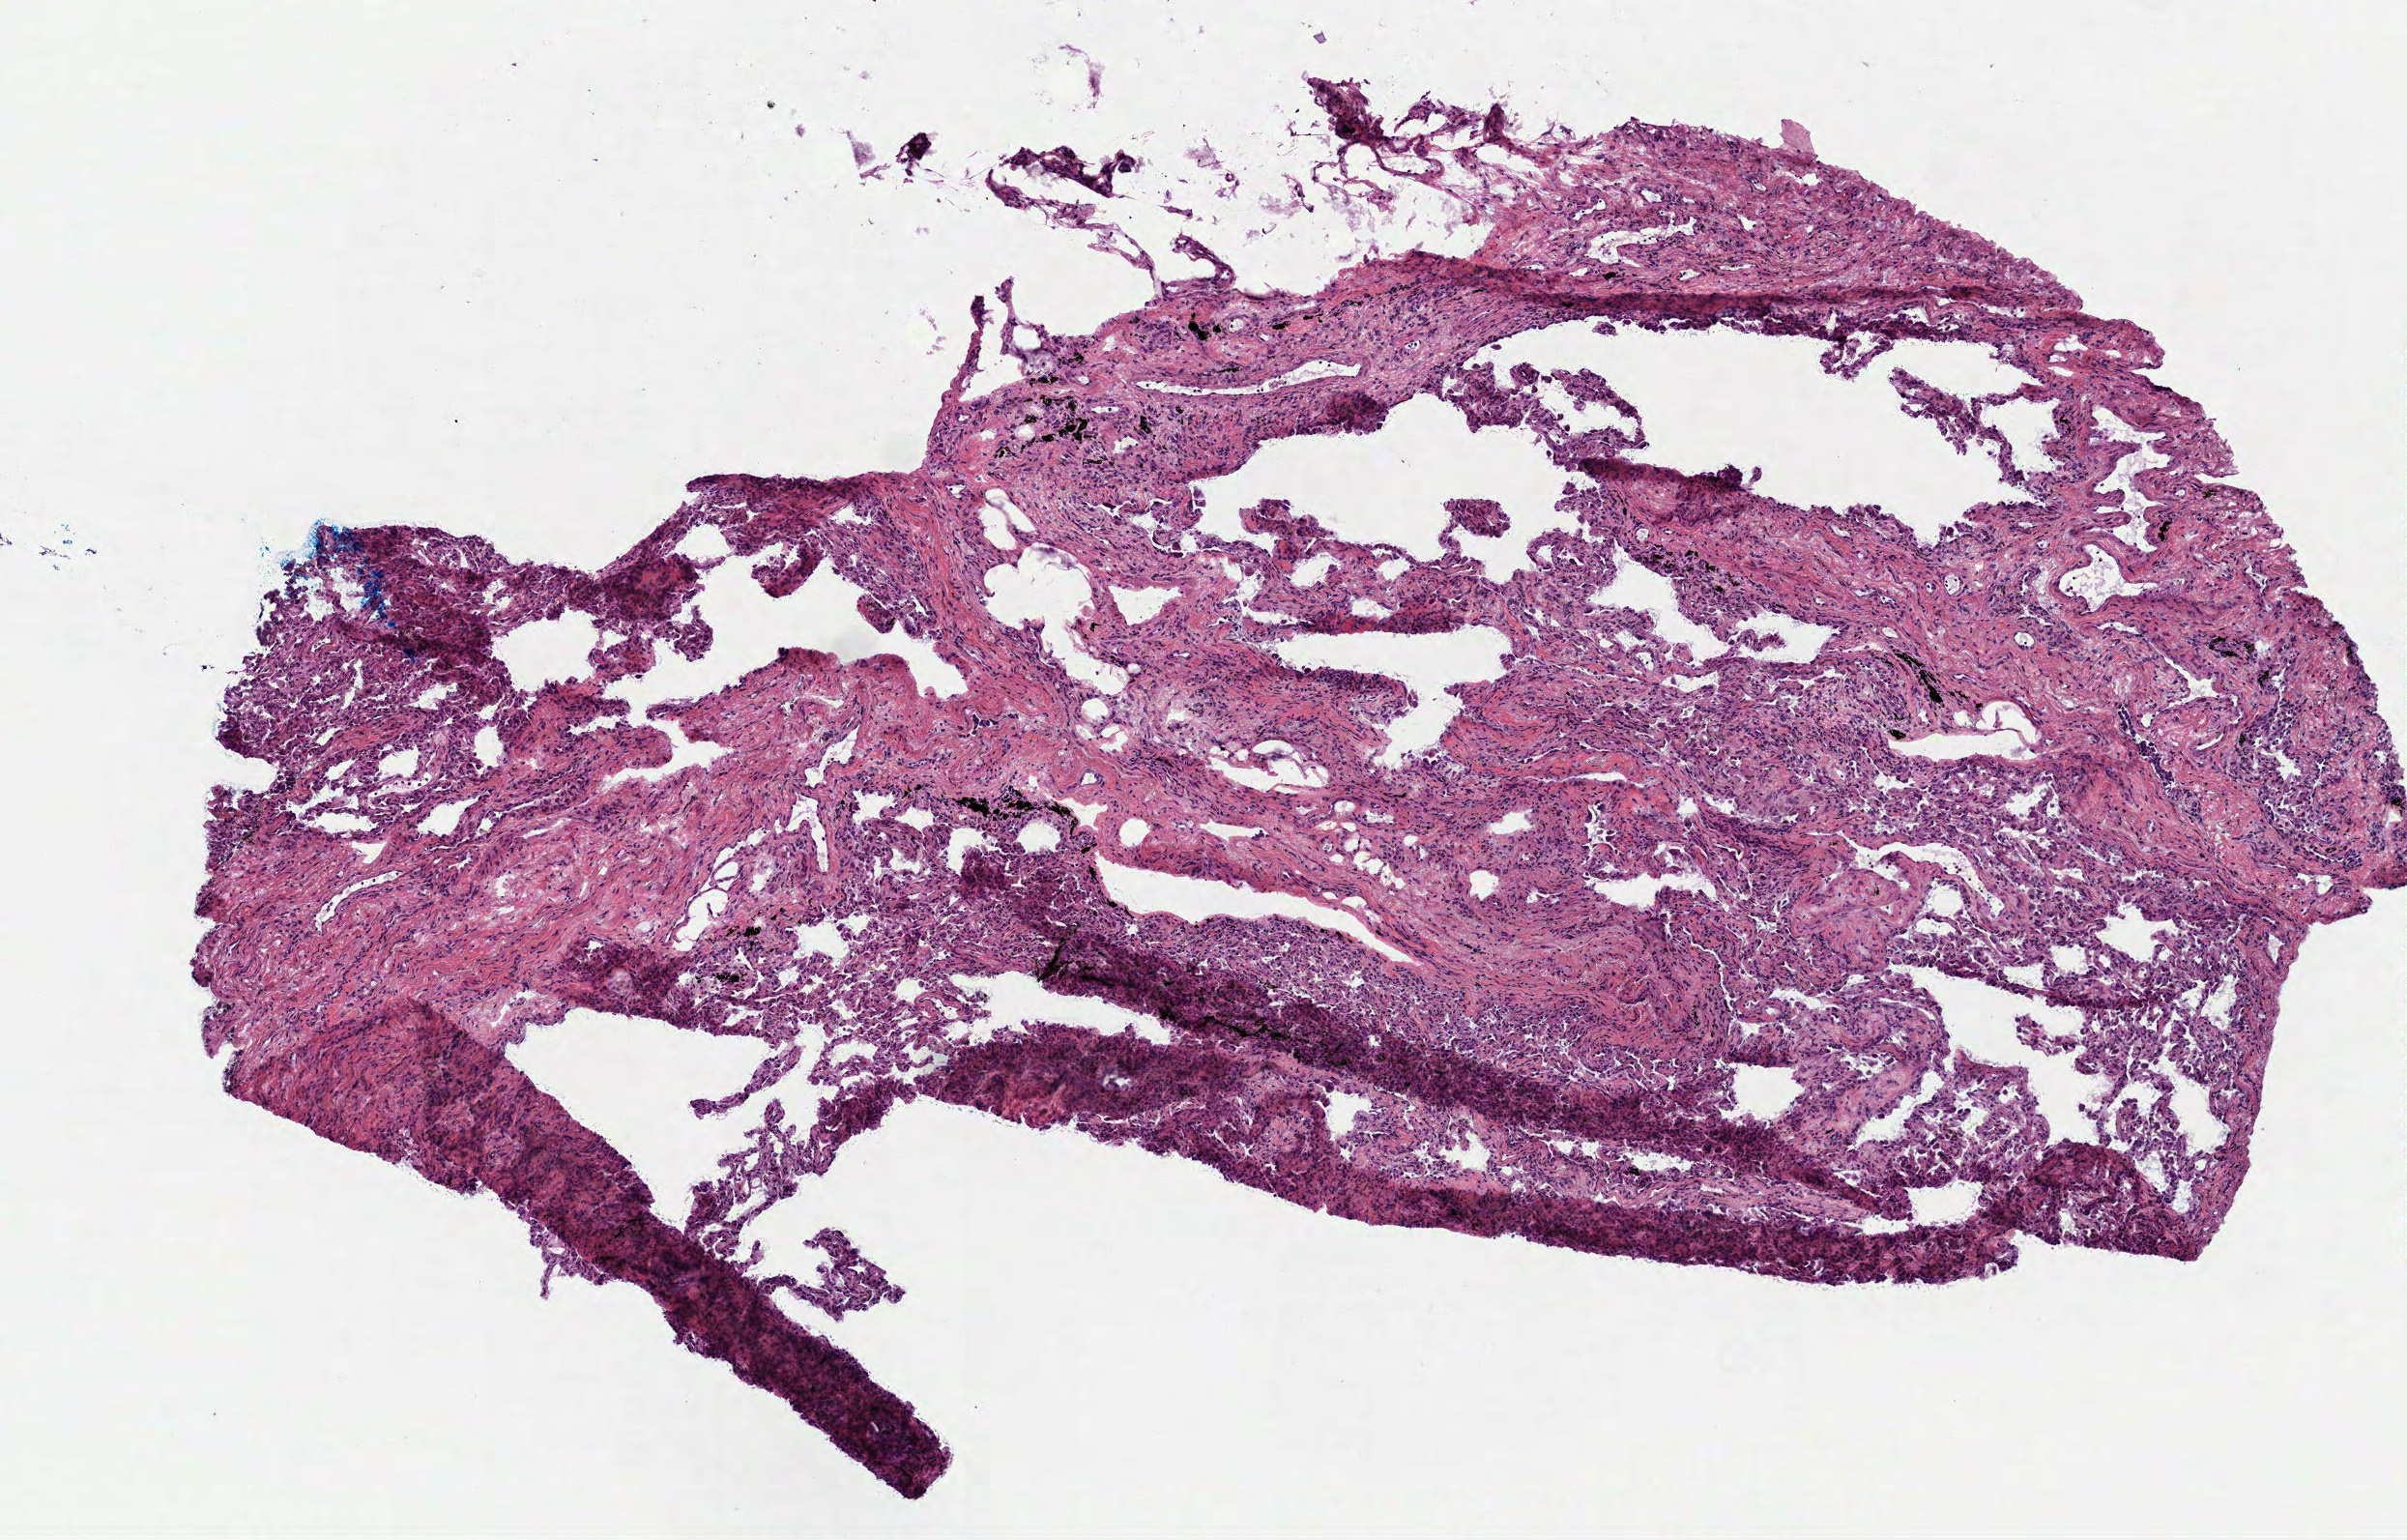
Whole-slide histology image, H&E-stained — a low-resolution overview of the entire scanned area, about 5.0 x 3.2 mm, frozen section, sample: solid tissue normal (non-tumour tissue), lung. Male, age 63 years at initial diagnosis.
This section: solid tissue normal sample (biorepository sample class). Patient diagnosis: Adenocarcinoma, NOS (lower lobe, lung).